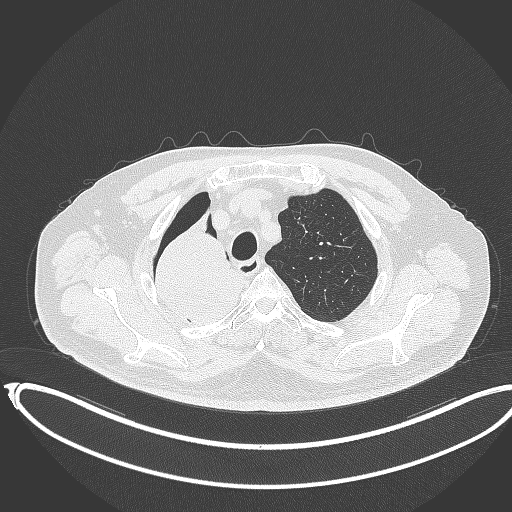
Chest CT, one axial slice. Slice 303 of 403 in the series (ordered by position). Lung window (W 1500 / L -600 HU). 1 mm slice thickness. 512 × 512 image matrix, field of view 436 × 436 mm. Male patient, age 68 years. From the clinical record (not read from this slice): clinical TNM (as recorded): T2a N0 M0.
Structures marked on this image (bounding box drawn by a radiologist):
- lung tumour (recorded histology: adenocarcinoma): bounding box [x1, y1, x2, y2] px = [151, 214, 248, 327]